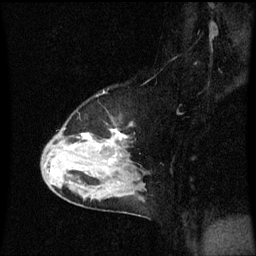
Breast MRI (dynamic contrast-enhanced), one sagittal slice. Position 43 of 60 along the scan axis. Dynamic contrast-enhanced series, image 2 of 3 at this slice position (ordered by acquisition). 1.5 T. TE 4.2 ms, TR 8.9 ms. 2 mm slice thickness. 256 × 256 image matrix. Patient: female, 50 years. From the clinical record (not read from this slice): setting: breast cancer imaged before/during neoadjuvant chemotherapy; receptor status: HR-positive, HER2-negative.
Structures marked on this image (semi-automatic segmentation, software-assisted and operator-edited):
- analysis volume of interest (the breast-tissue region the enhancement analysis was run in; not a lesion): bounding box (x1, y1, x2, y2) in pixels: (43, 128, 147, 207)
- tumour enhancement mask (voxels above the 70 % enhancement threshold inside the analysis volume of interest): (75, 134, 115, 163)